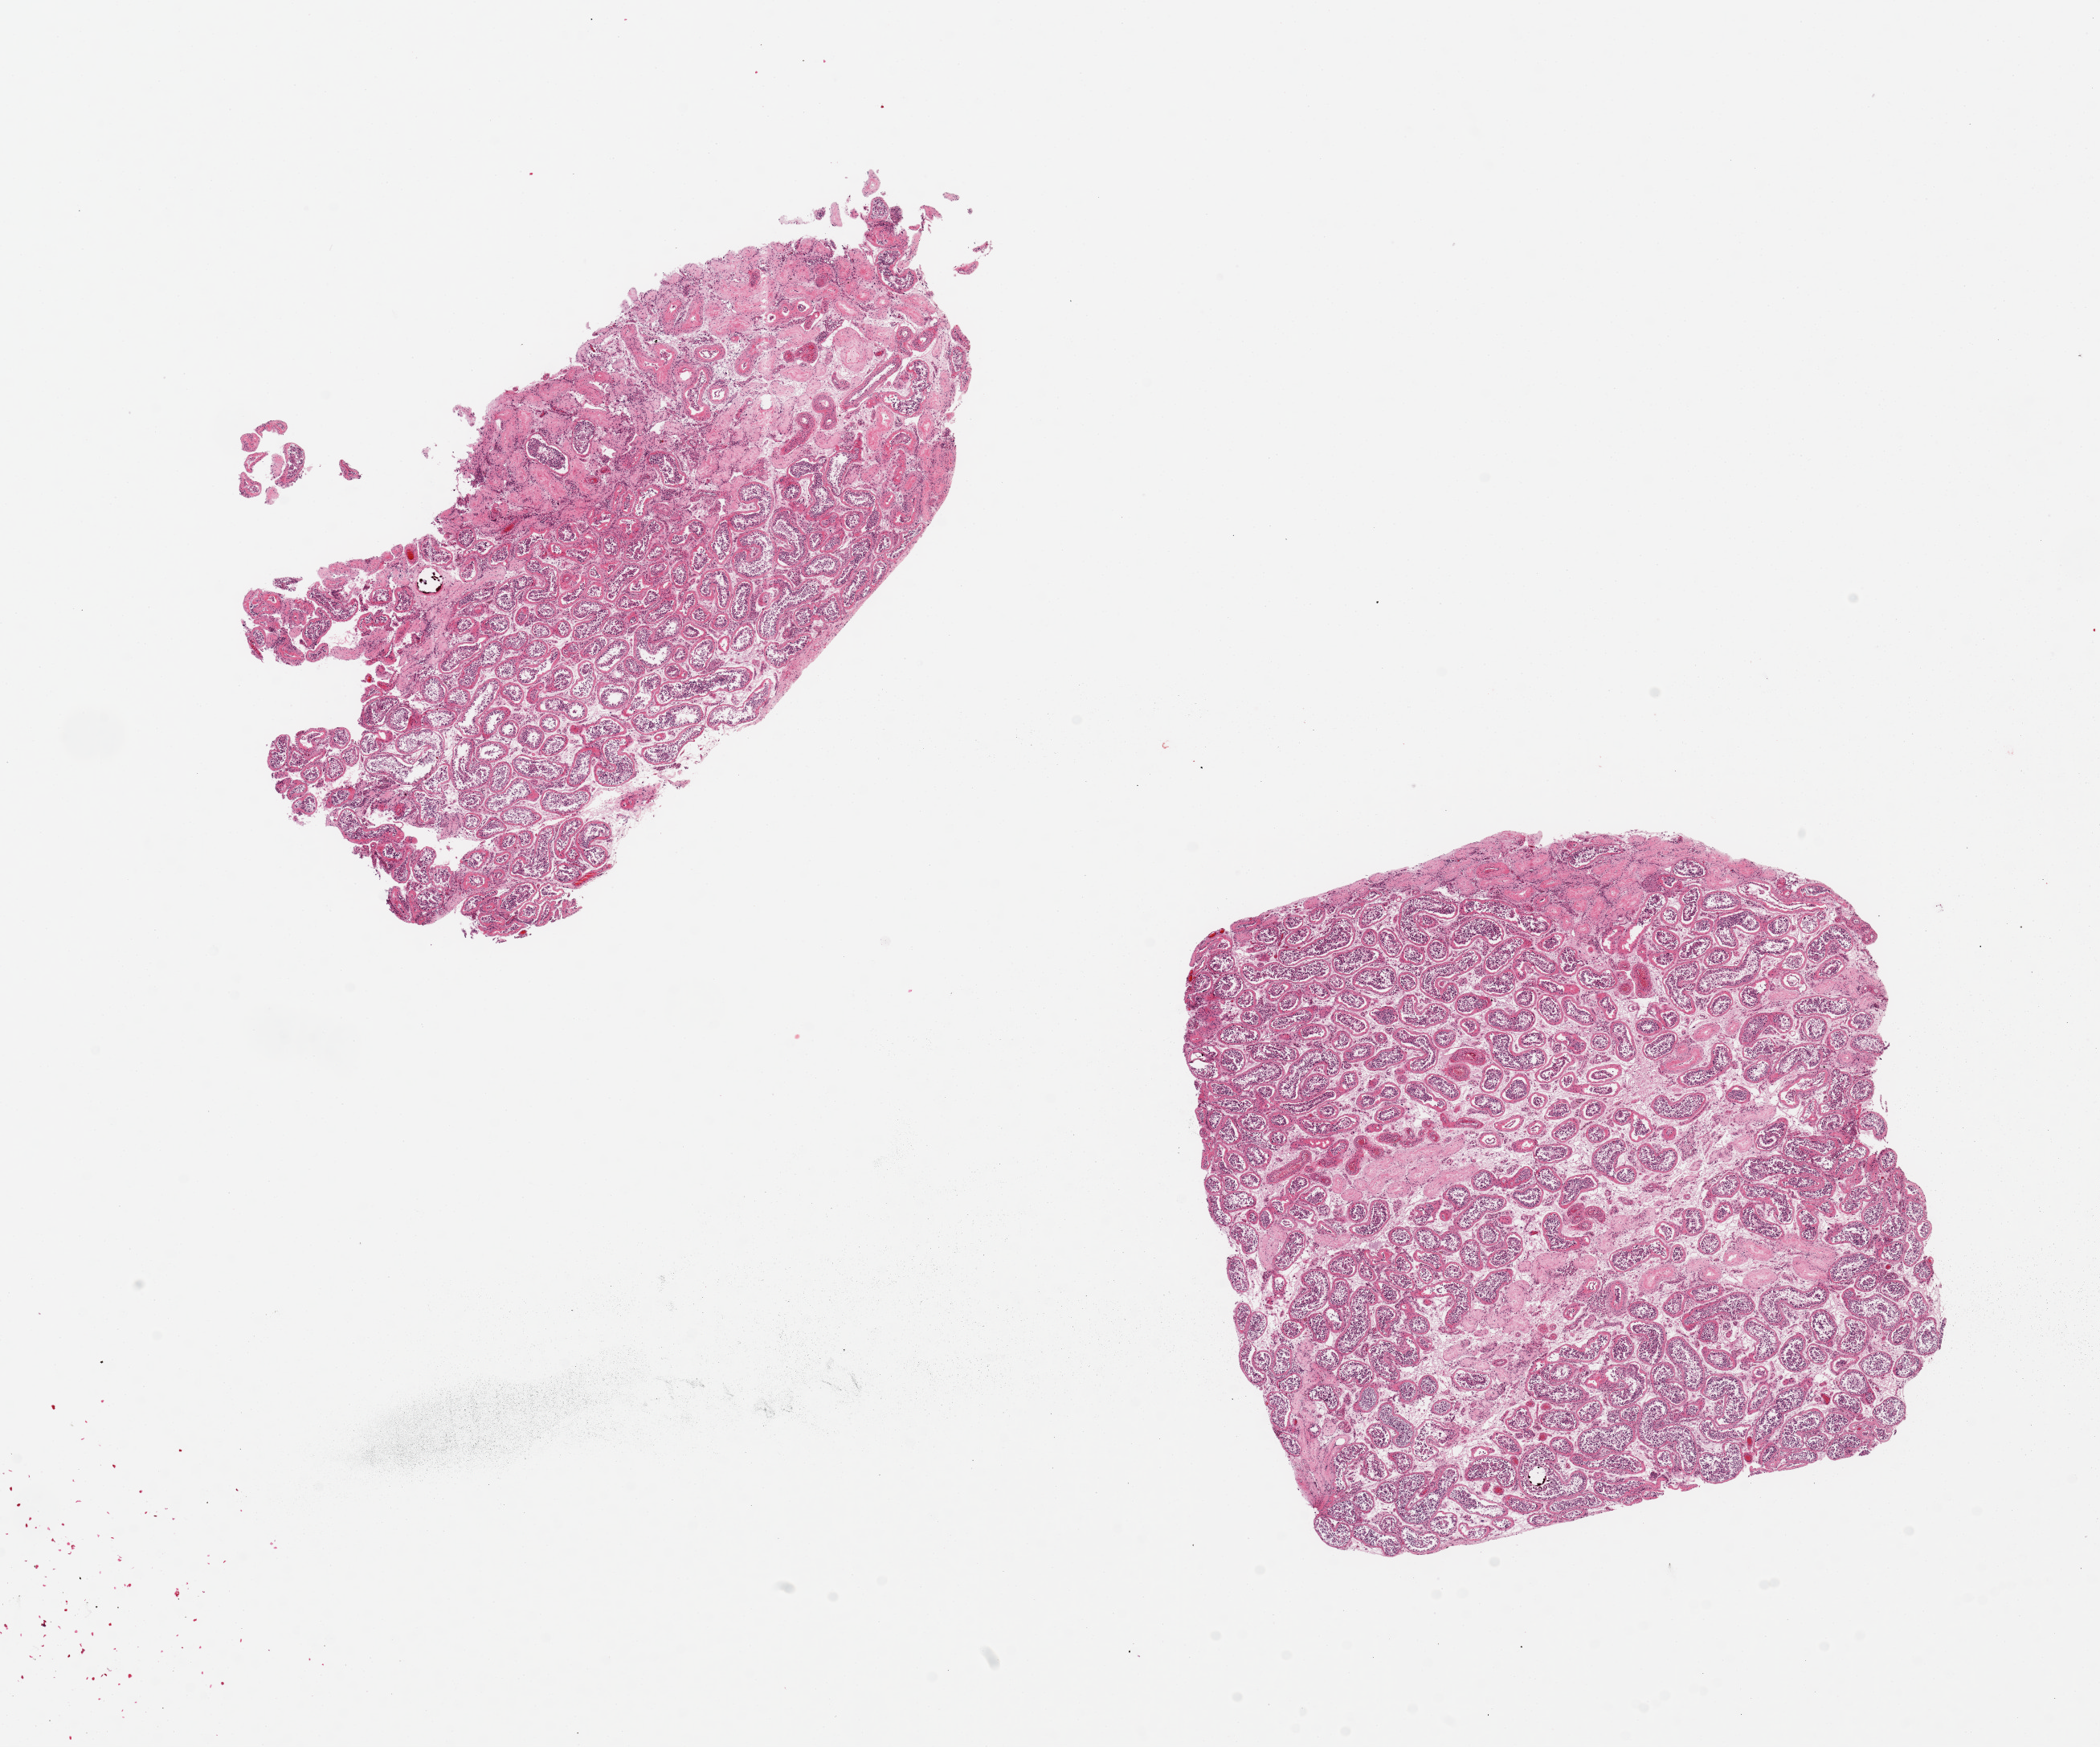
Whole-slide image, hematoxylin and eosin (H&E) stain, brightfield — whole scanned area (about 20.7 x 17.2 mm) shown as a low-resolution overview; PAXgene-fixed, paraffin-embedded tissue; section of testis (target tissue); donor tissue sample. Donor: male.
Reviewer comment on this tissue sample: 2 pieces, 4.5x8 & 6.6x6mm; moderate patchy tubular fibrosis; decreased spermatogenesis.